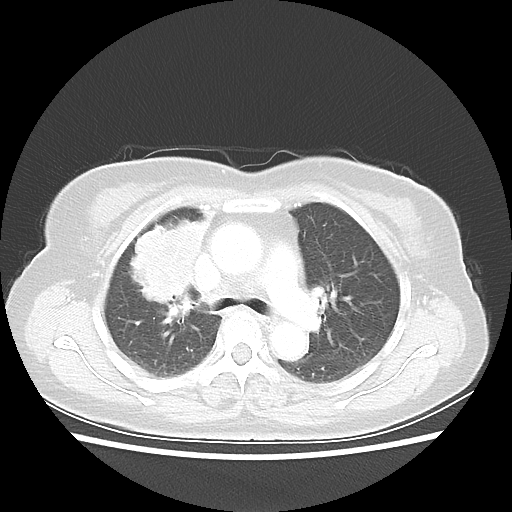
Chest CT, one axial slice. Position 35 of 55 along the scan axis. Lung window (W 1500 / L -600 HU). 5 mm slice thickness. 512 × 512 image matrix. Female patient, age 62 years. Case-level facts recorded for this patient, not image findings: clinical TNM (as recorded): T4 N3 M0.
Outlined on this slice (rectangle marked by the reading radiologist):
- lung tumour (recorded histology: squamous cell carcinoma): bounding box [x1, y1, x2, y2] px = [121, 203, 217, 309]